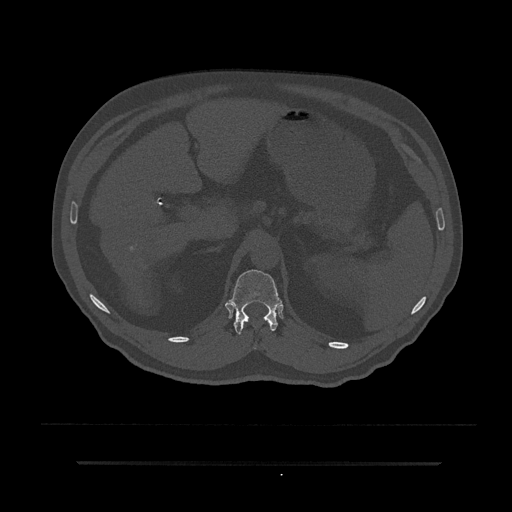
CT including the spine, one axial slice; position 221 of 797 along the scan axis; reconstruction kernel Br40s/3; 120 kVp; bone window (W 1800 / L 400 HU); 0.5 mm slice thickness; 512 × 512 image matrix, field of view 464 × 464 mm. Male patient, age 59 years. Case-level facts recorded for this patient, not image findings: primary cancer: bile ducts; vertebrae with lytic lesions (as recorded): T10.
Outlined on this slice (semi-automatically segmented with operator editing):
- T12 vertebra: bounding box (x1, y1, x2, y2) in pixels: (228, 269, 282, 335)